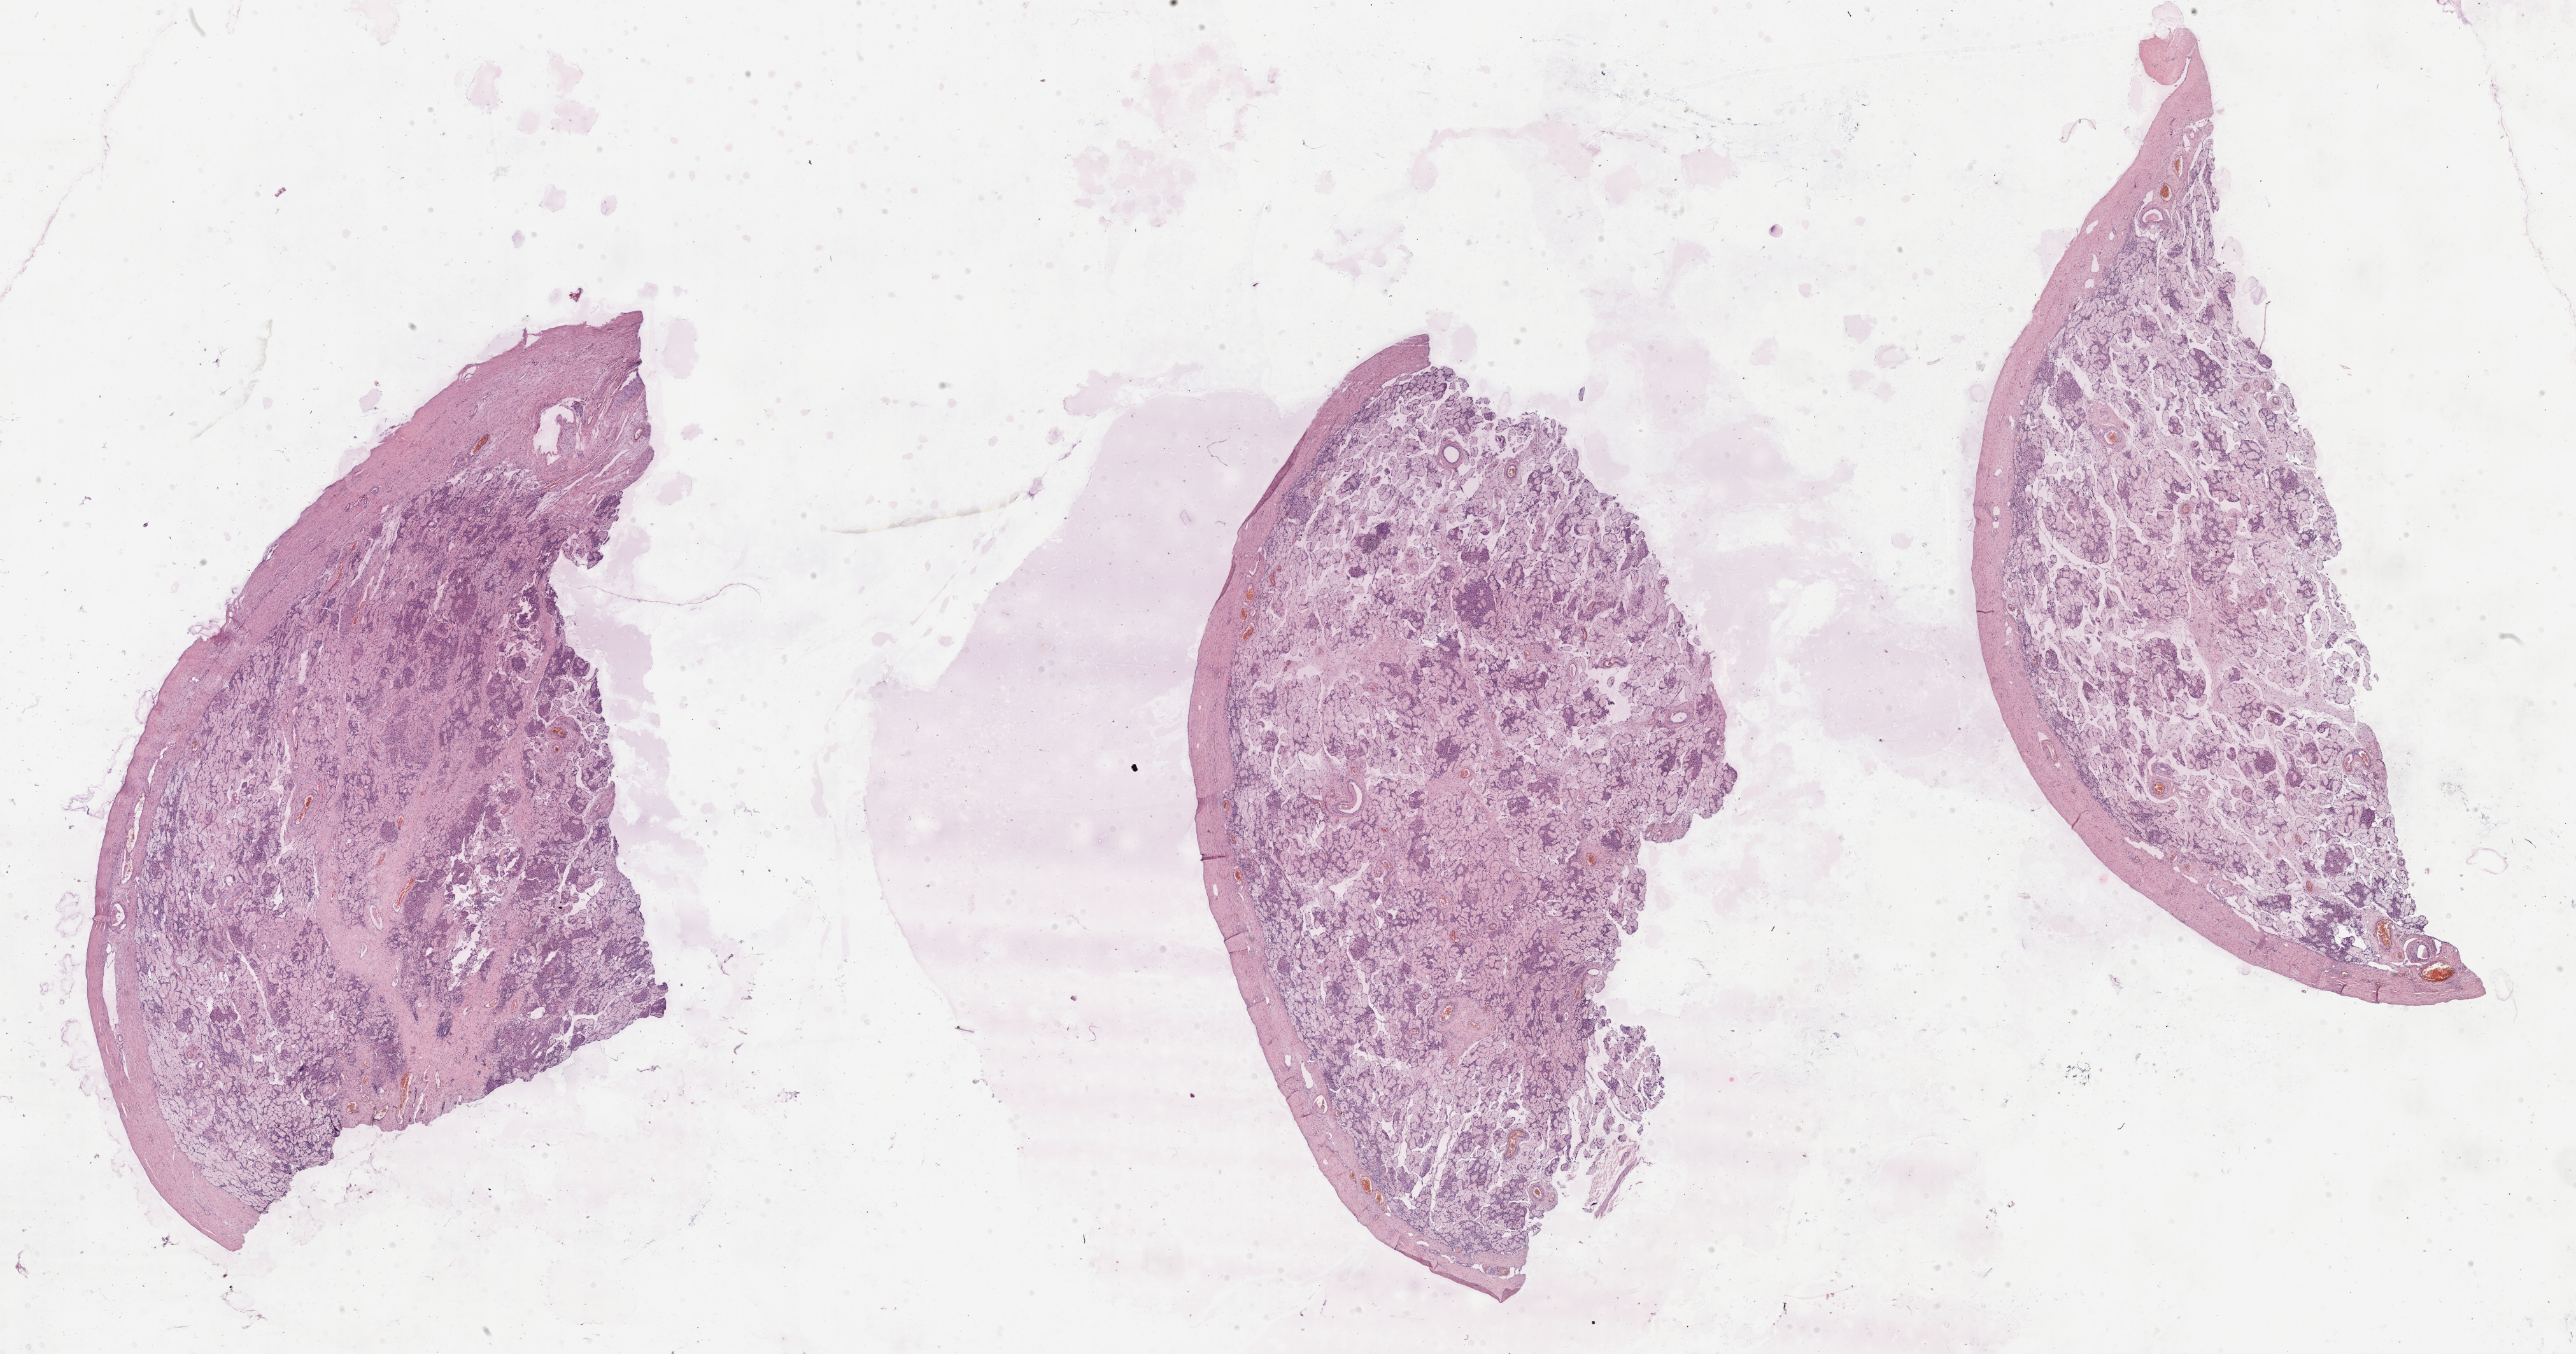
H&E whole-slide image — low-resolution overview of the scanned area, about 32.7 x 17.2 mm; formalin-fixed paraffin-embedded (FFPE) diagnostic section; sample: primary tumour, skin. Female, age 76 years at initial diagnosis.
Histologic diagnosis: Malignant melanoma, NOS. AJCC pathologic stage: IIIC (7th edition).